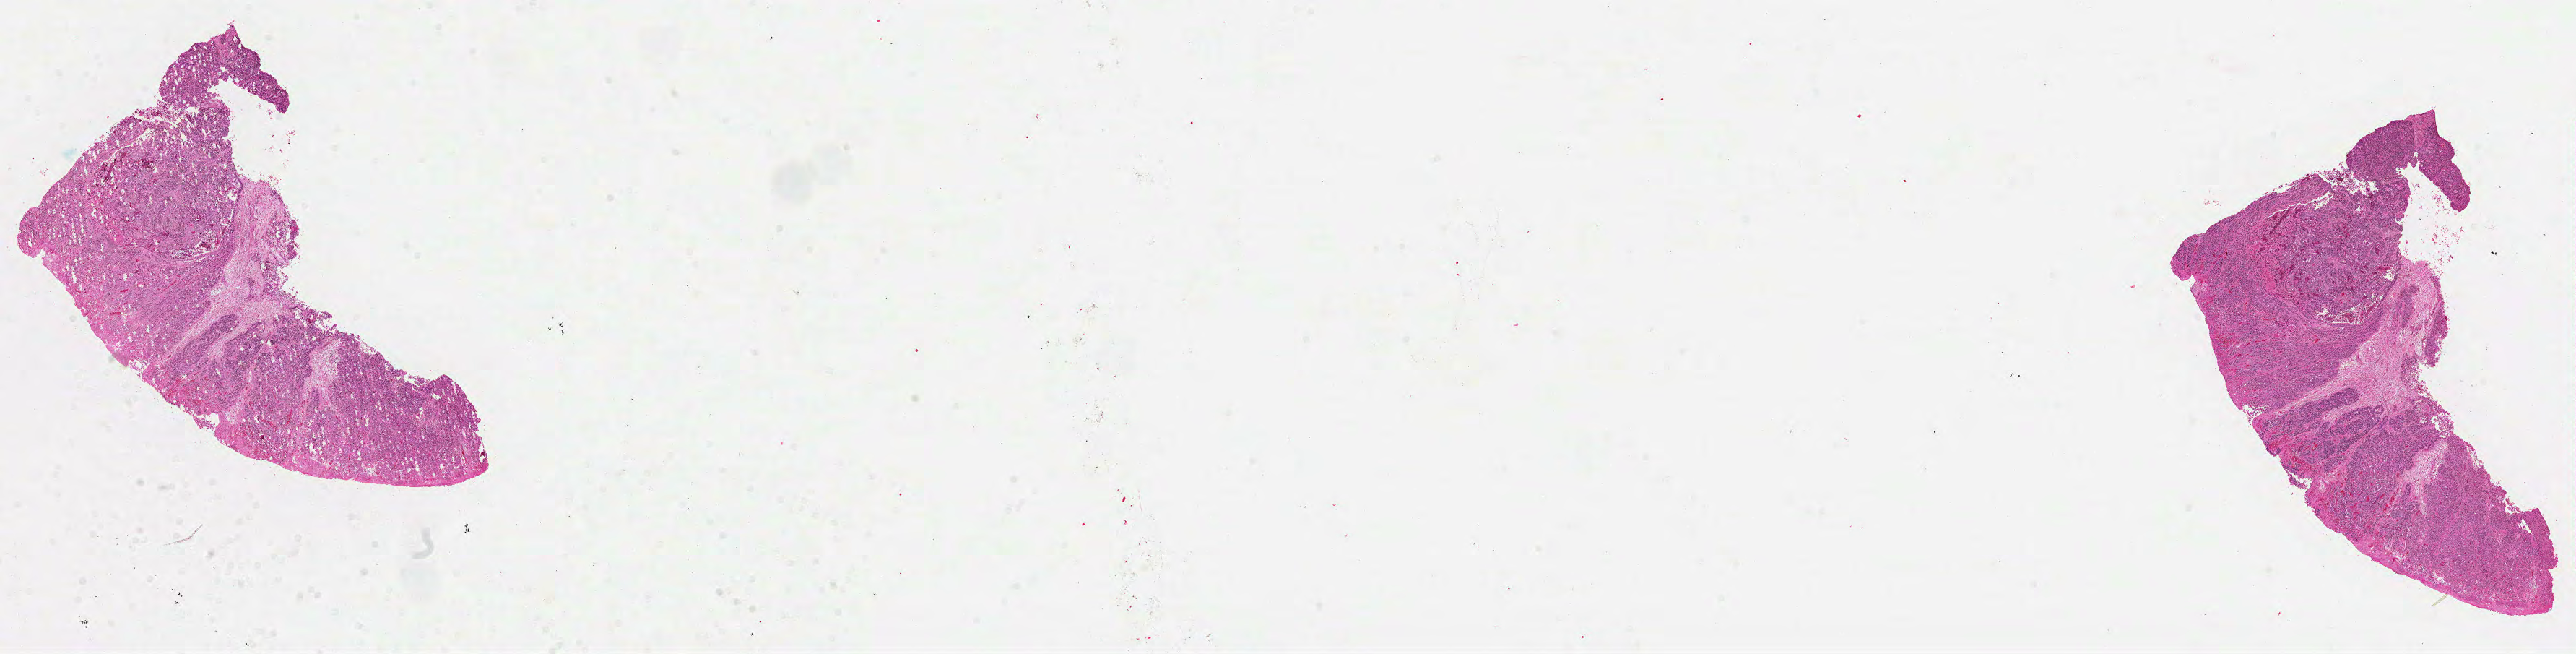
Hematoxylin and eosin (H&E) stained whole-slide image — a low-resolution overview of the entire scanned area, about 28.8 x 7.3 mm (slide scanned at 40x); formalin-fixed paraffin-embedded (FFPE) diagnostic section; sample: primary tumour, stomach. Male patient; age at initial diagnosis 79 years. Histologic grade: G2 (moderately differentiated).
* AJCC pathologic stage: IA (4th edition)
* pathologic diagnosis: Adenocarcinoma, NOS (gastric antrum)
* lymph nodes positive (case pathology): 0 of 17 examined